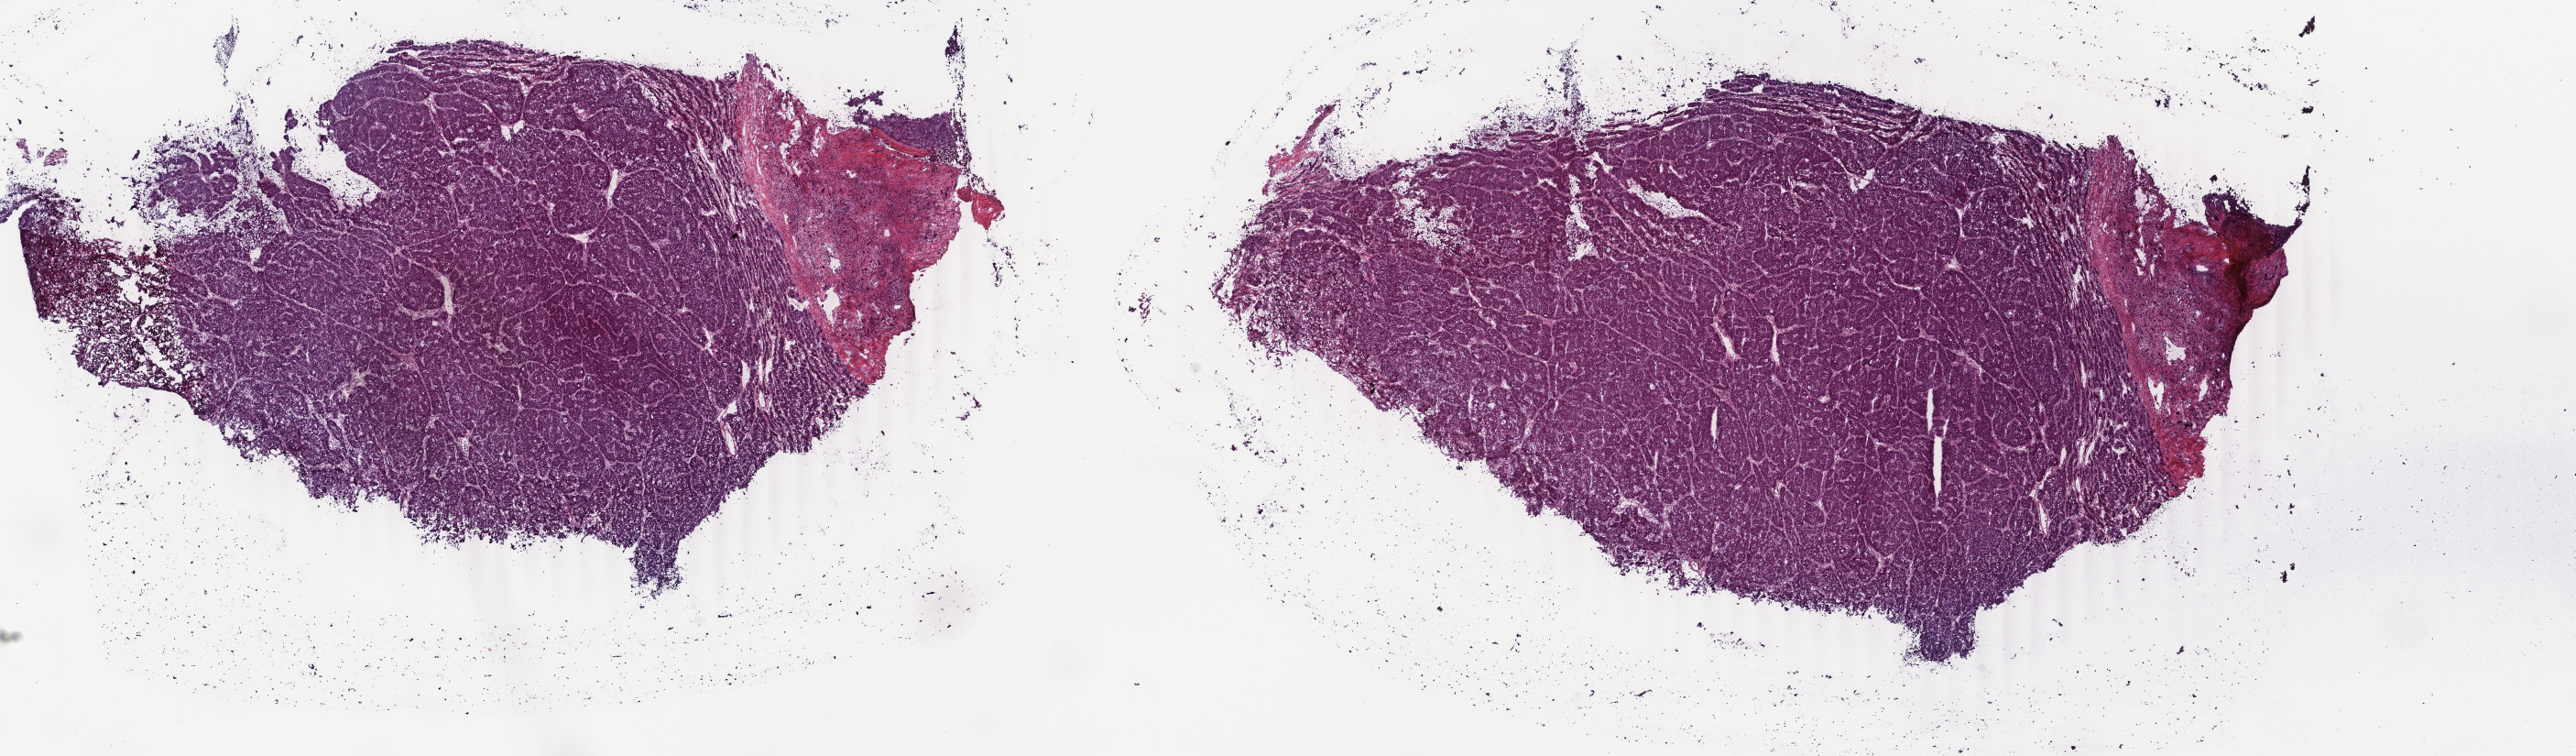
Digitized H&E-stained tissue section (whole slide) — a low-resolution overview of the entire scanned area, about 22.4 x 6.6 mm (acquisition: 40x scan), frozen section from the top of the tissue portion, liver, primary tumour sample. Patient: male, age at initial diagnosis 53 years. Histologic grade: G2 (moderately differentiated). Pathologist review of this section (percent, as recorded): tumour cells 90%, tumour nuclei 90%, normal cells 4%, stromal cells 6%, necrosis 0%. Infiltration values recorded for this section: lymphocyte infiltration 1%, monocyte infiltration 0%, neutrophil infiltration 0%.
AJCC pathologic stage: IIIA (5th edition). TNM: T3 N0 M0. Diagnosis: Hepatocellular carcinoma, NOS.